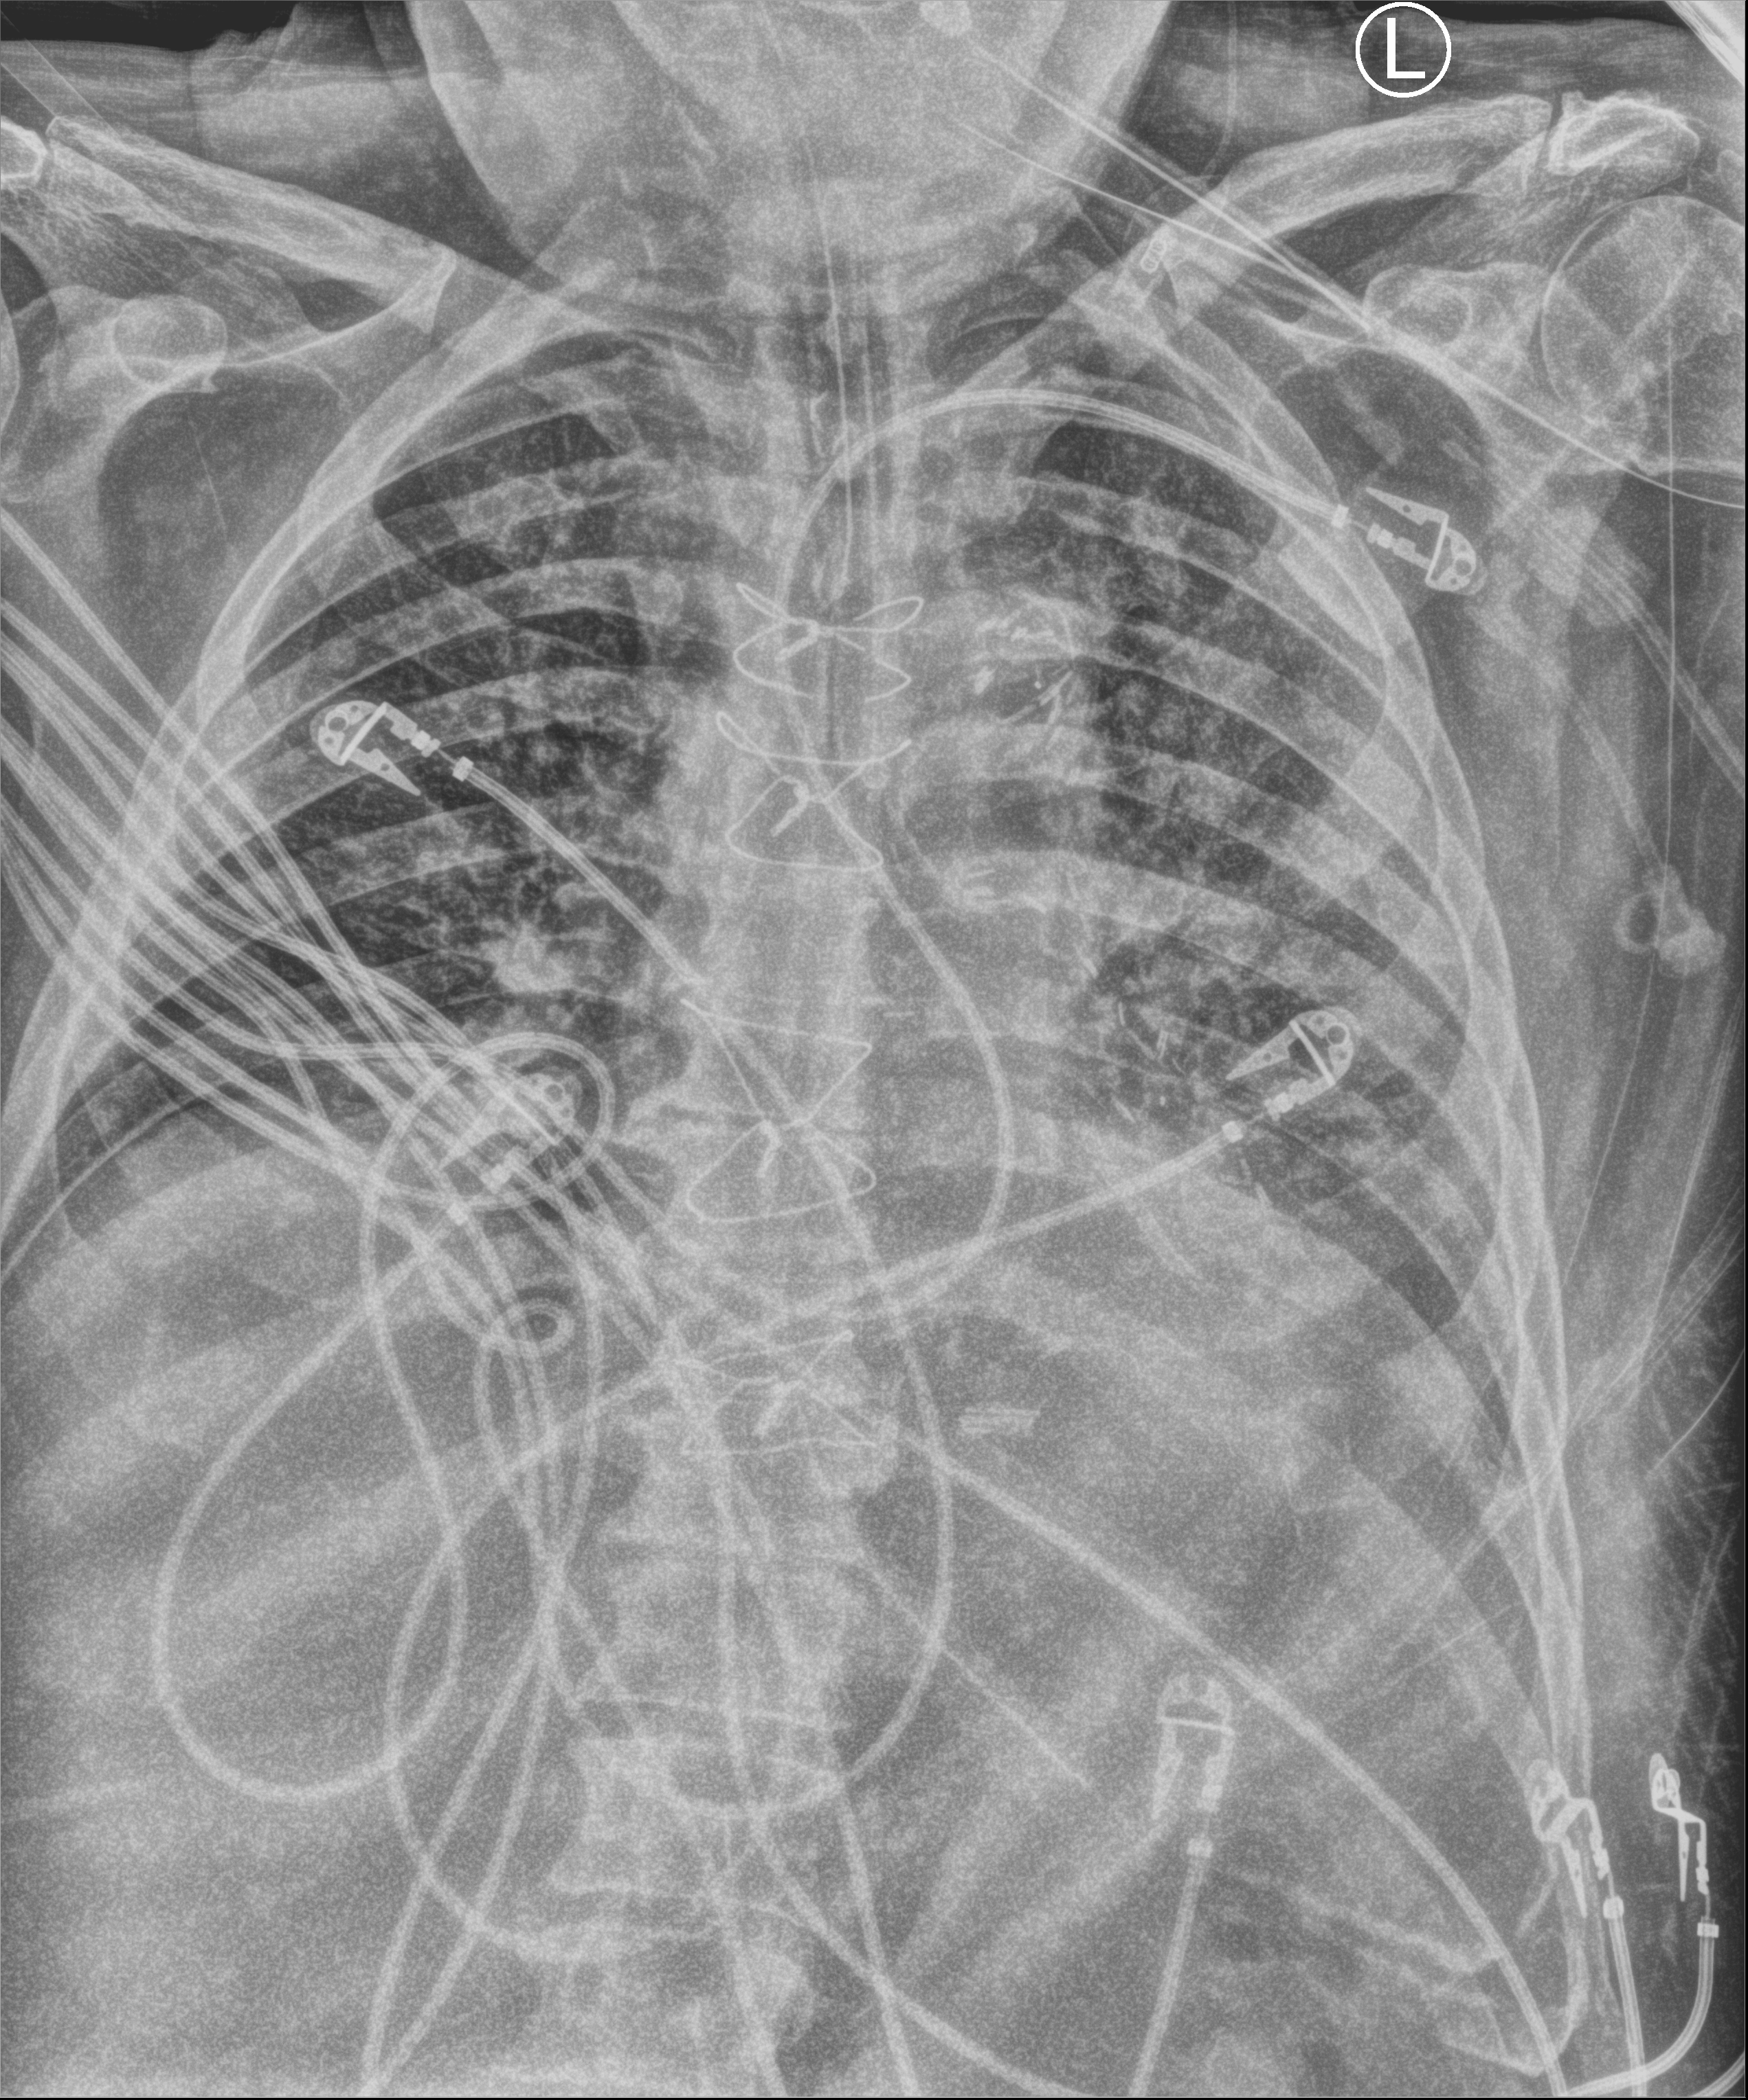
Chest X-ray (portable). Male patient hospitalised with COVID-19, age 60–74 years.
Admission-level facts for this patient (not findings on this image; timing relative to this image not recorded): admitted to intensive care during this hospital stay: yes; length of hospital stay: 16 days; mechanically ventilated during this hospital stay: yes.